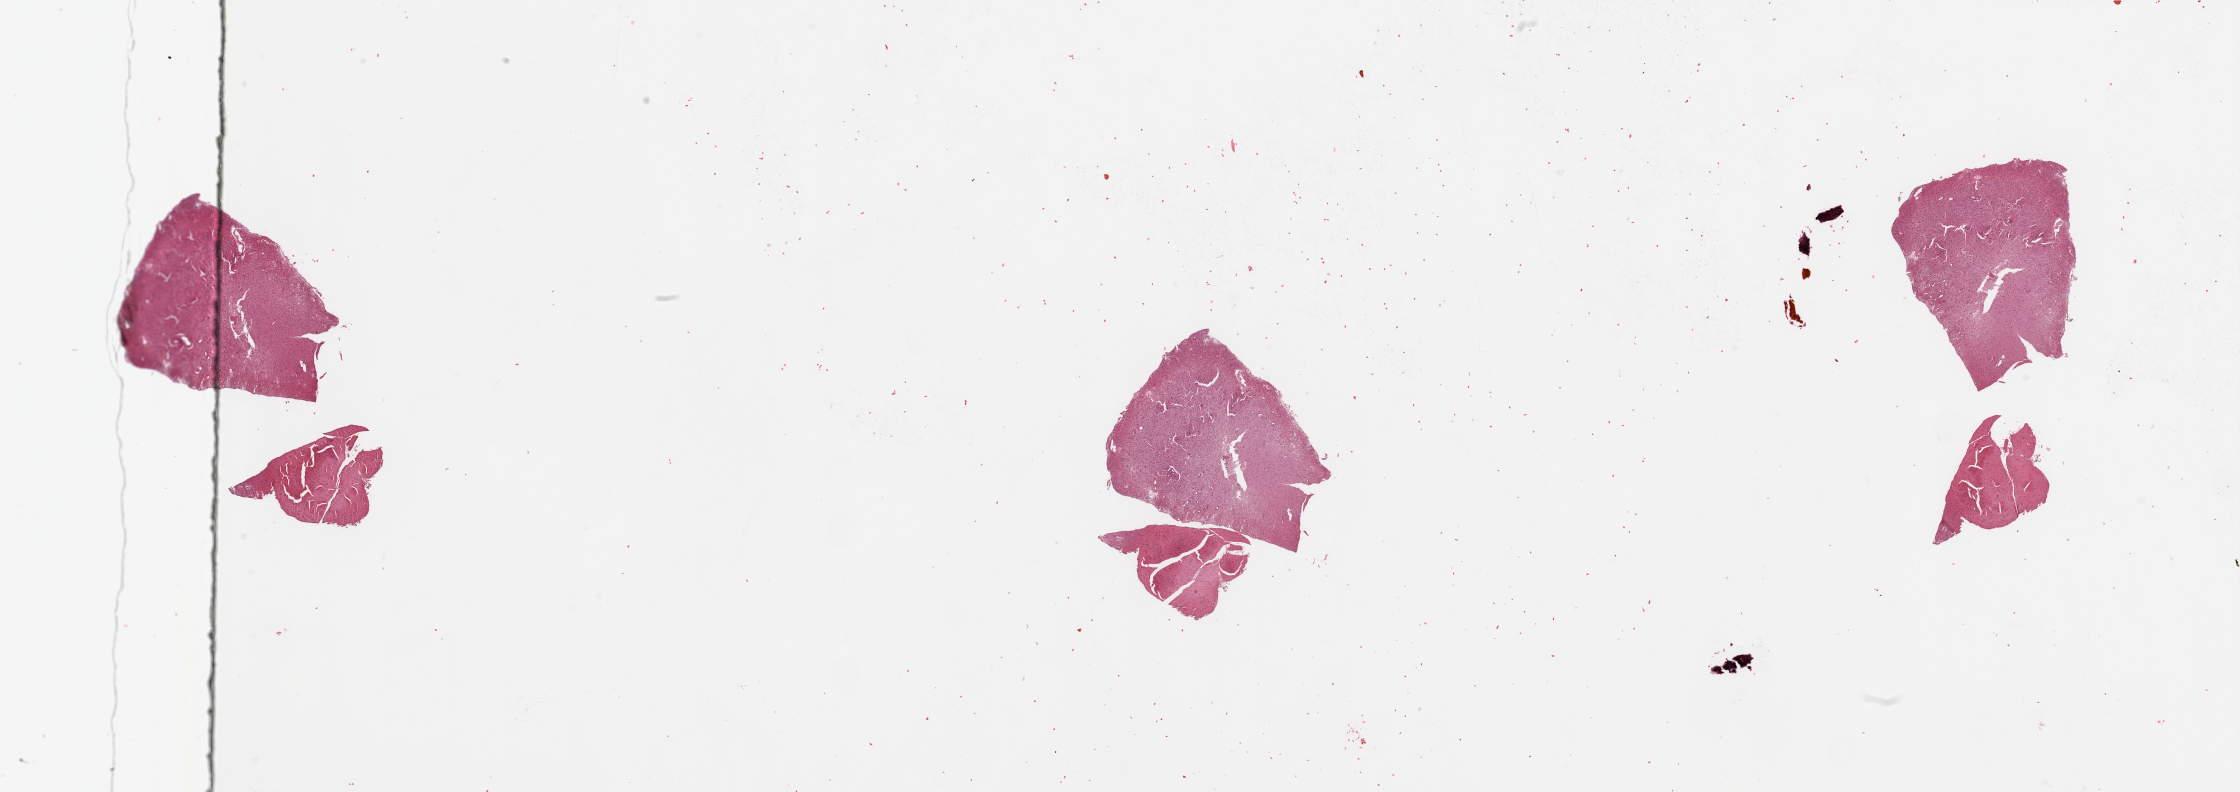
Digitized Hematoxylin and eosin (H&E) stained tissue section (whole slide), low-resolution overview of the scanned area, about 35.4 x 12.5 mm (from a 20x scan); tumour tissue sample, brain. 73-year-old male patient.
- patient diagnosis (cohort enrolment): glioblastoma multiforme (brain)
- primary tumour site (as recorded): temporal lobe